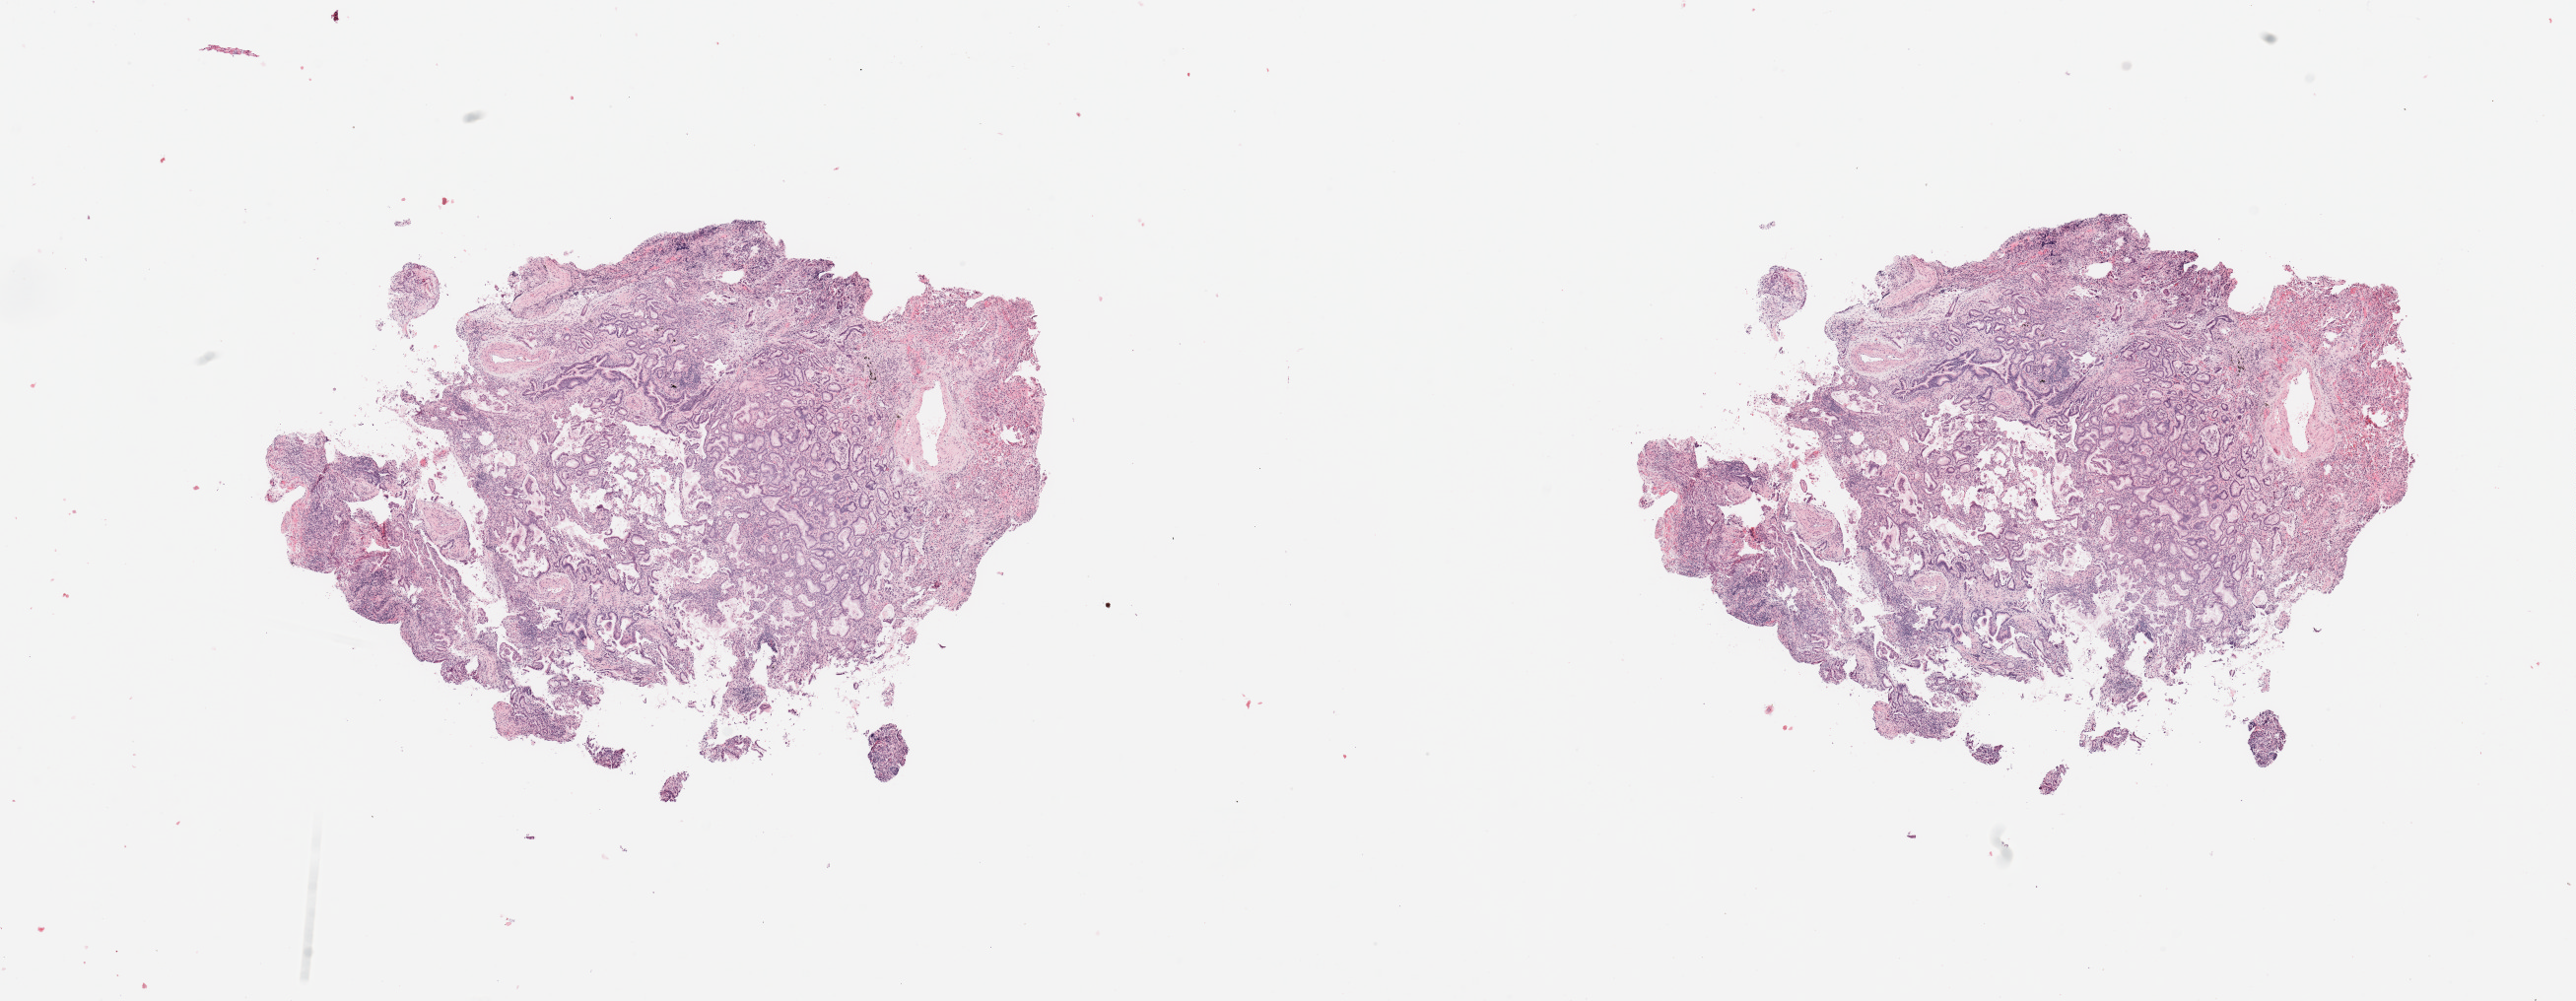
Digitized Hematoxylin and eosin (H&E) stained tissue section (whole slide) — a low-resolution overview of the entire scanned area, about 20.7 x 8.0 mm. Tumour tissue sample, lung. 46-year-old male patient. Histologic grade: G2 (moderately differentiated).
Diagnosis: Adenocarcinoma, NOS.